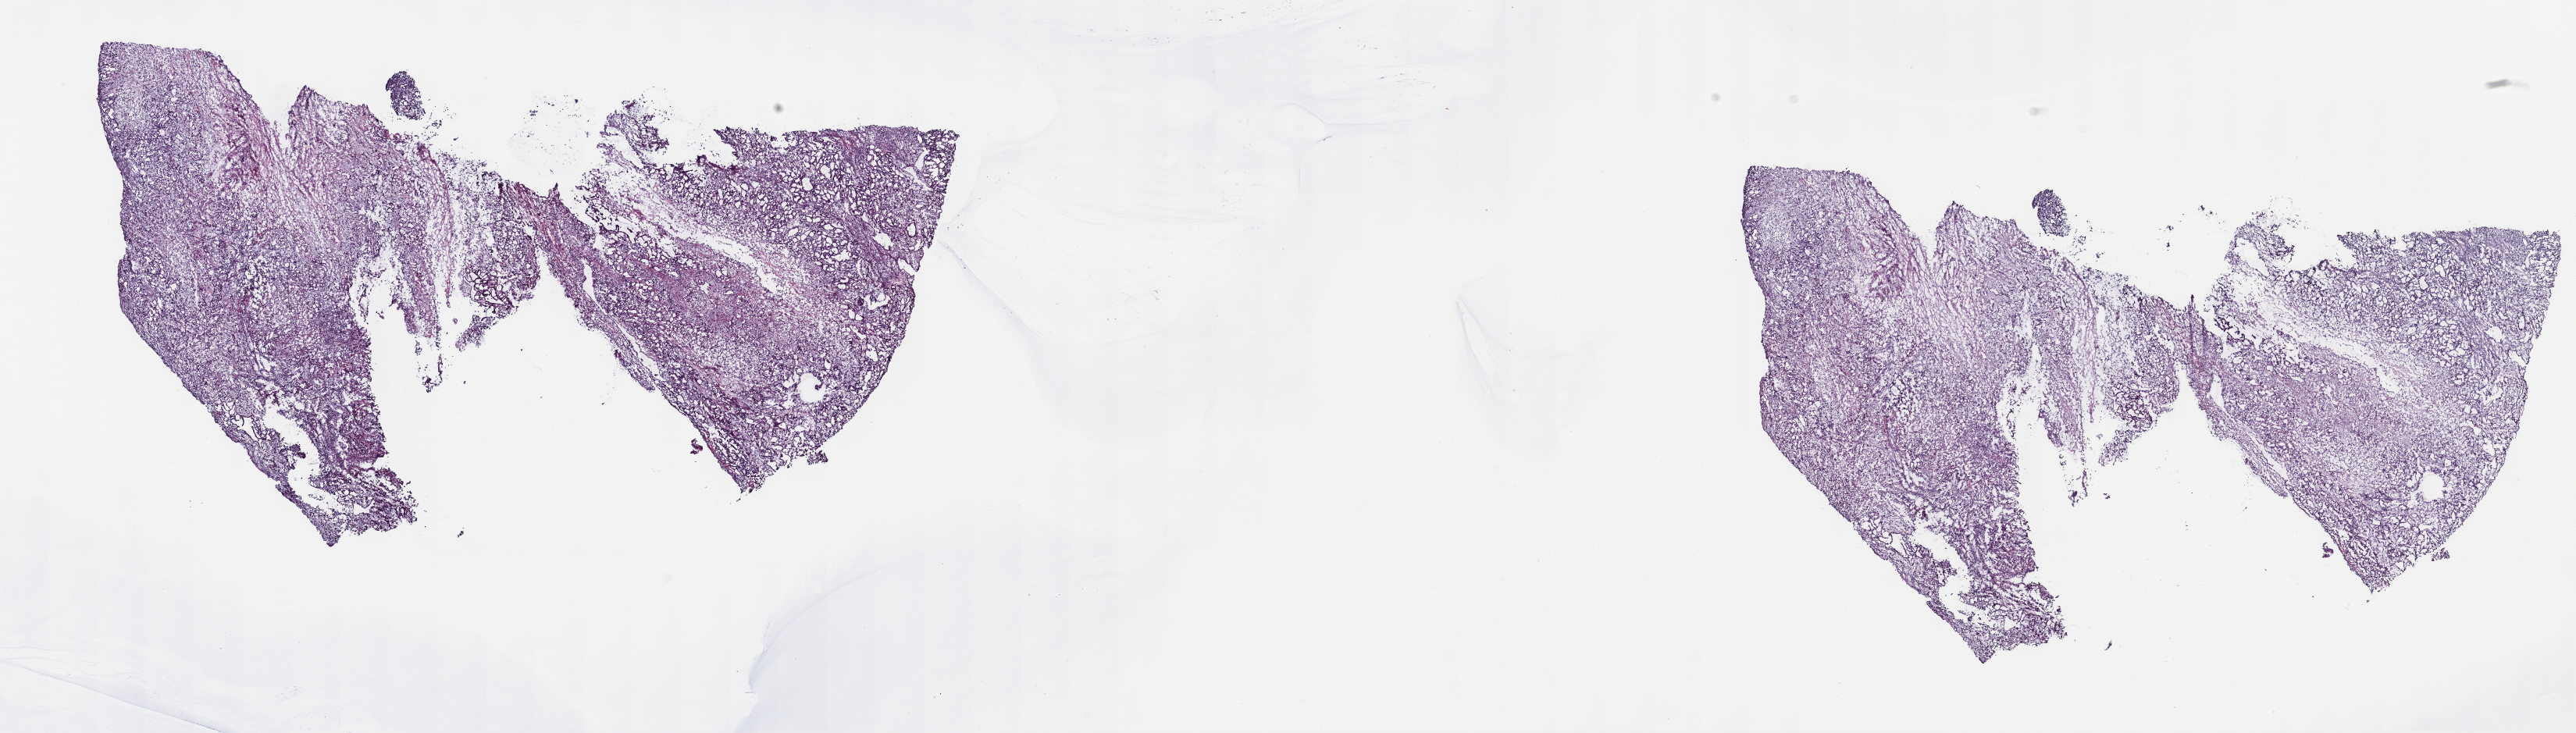
H&E-stained whole-slide image, whole scanned area (about 26.7 x 7.6 mm, acquisition: 40x scan) shown as a low-resolution overview. Frozen section. Primary tumour sample from the mesothelium. Male, age 61 years at initial diagnosis. Slide review estimates, as recorded: tumour cells 90%, tumour nuclei 90%, normal cells 0%, stromal cells 5%, necrosis 5%. Infiltration values recorded for this section: lymphocyte infiltration 60%, monocyte infiltration 10%, neutrophil infiltration 10%.
- pathologic diagnosis: Mesothelioma, biphasic, malignant (pleura, NOS)
- laterality: right
- AJCC pathologic stage: I